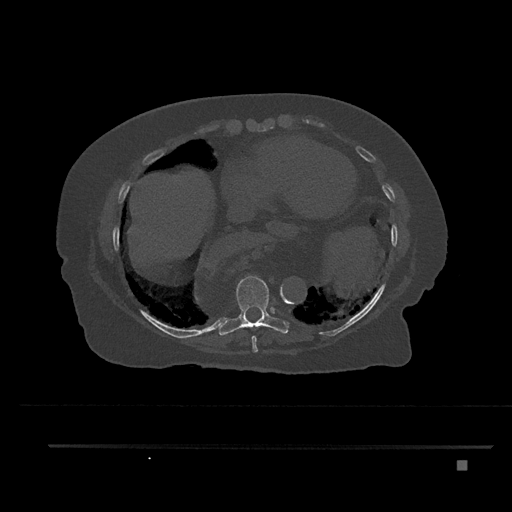
CT including the spine, one axial slice; position 407 of 797 along the scan axis; reconstruction kernel Br40s/3; bone window (W 1800 / L 400 HU); 0.5 mm slice thickness; 512 × 512 image matrix, field of view 437 × 437 mm. Female patient, age 76 years. From the clinical record (not read from this slice): primary cancer: lung; vertebrae with lytic lesions (as recorded): T11, L3.
Annotated regions visible in this slice (semi-automatic segmentation, software-assisted and operator-edited):
- T8 vertebra: bounding box (x1, y1, x2, y2) in pixels: (251, 336, 258, 352)
- T9 vertebra: (216, 276, 289, 336)